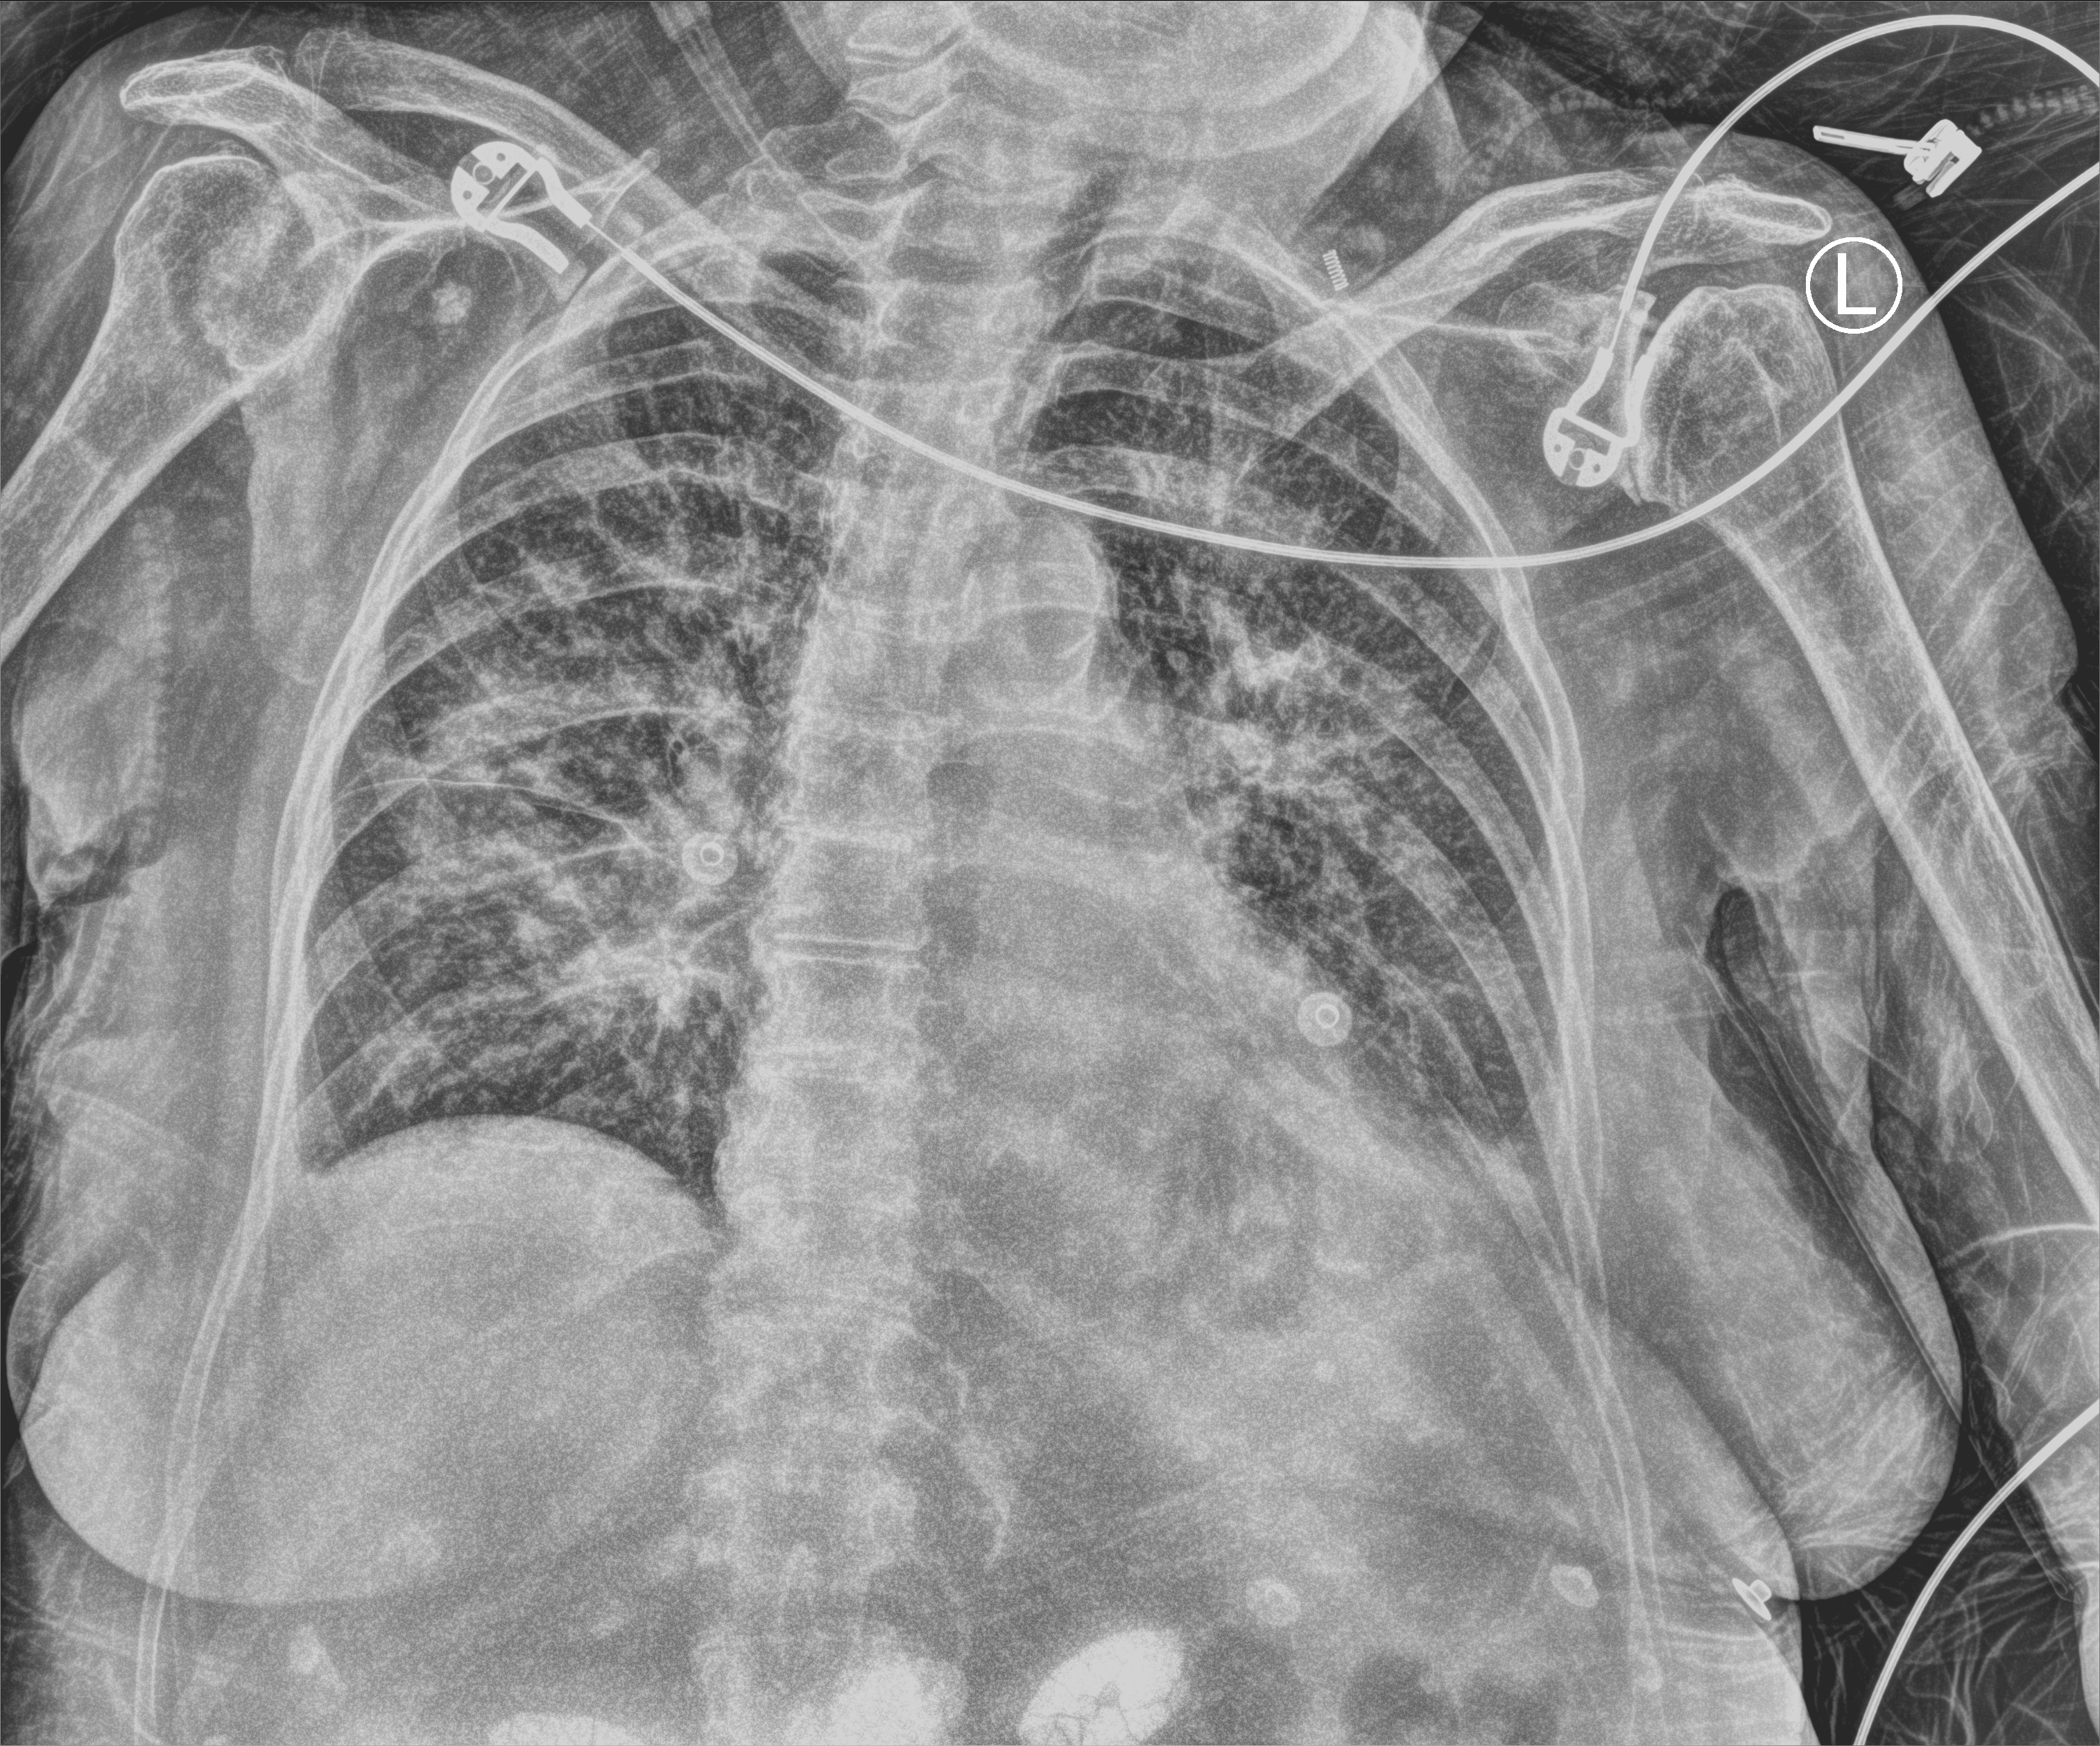
Bedside chest radiograph (computed radiography). Patient hospitalised with COVID-19; female, aged 75–90 years.
Hospital-stay facts (about this admission, not read from this image; timing relative to this image not recorded): mechanically ventilated during this hospital stay: no.